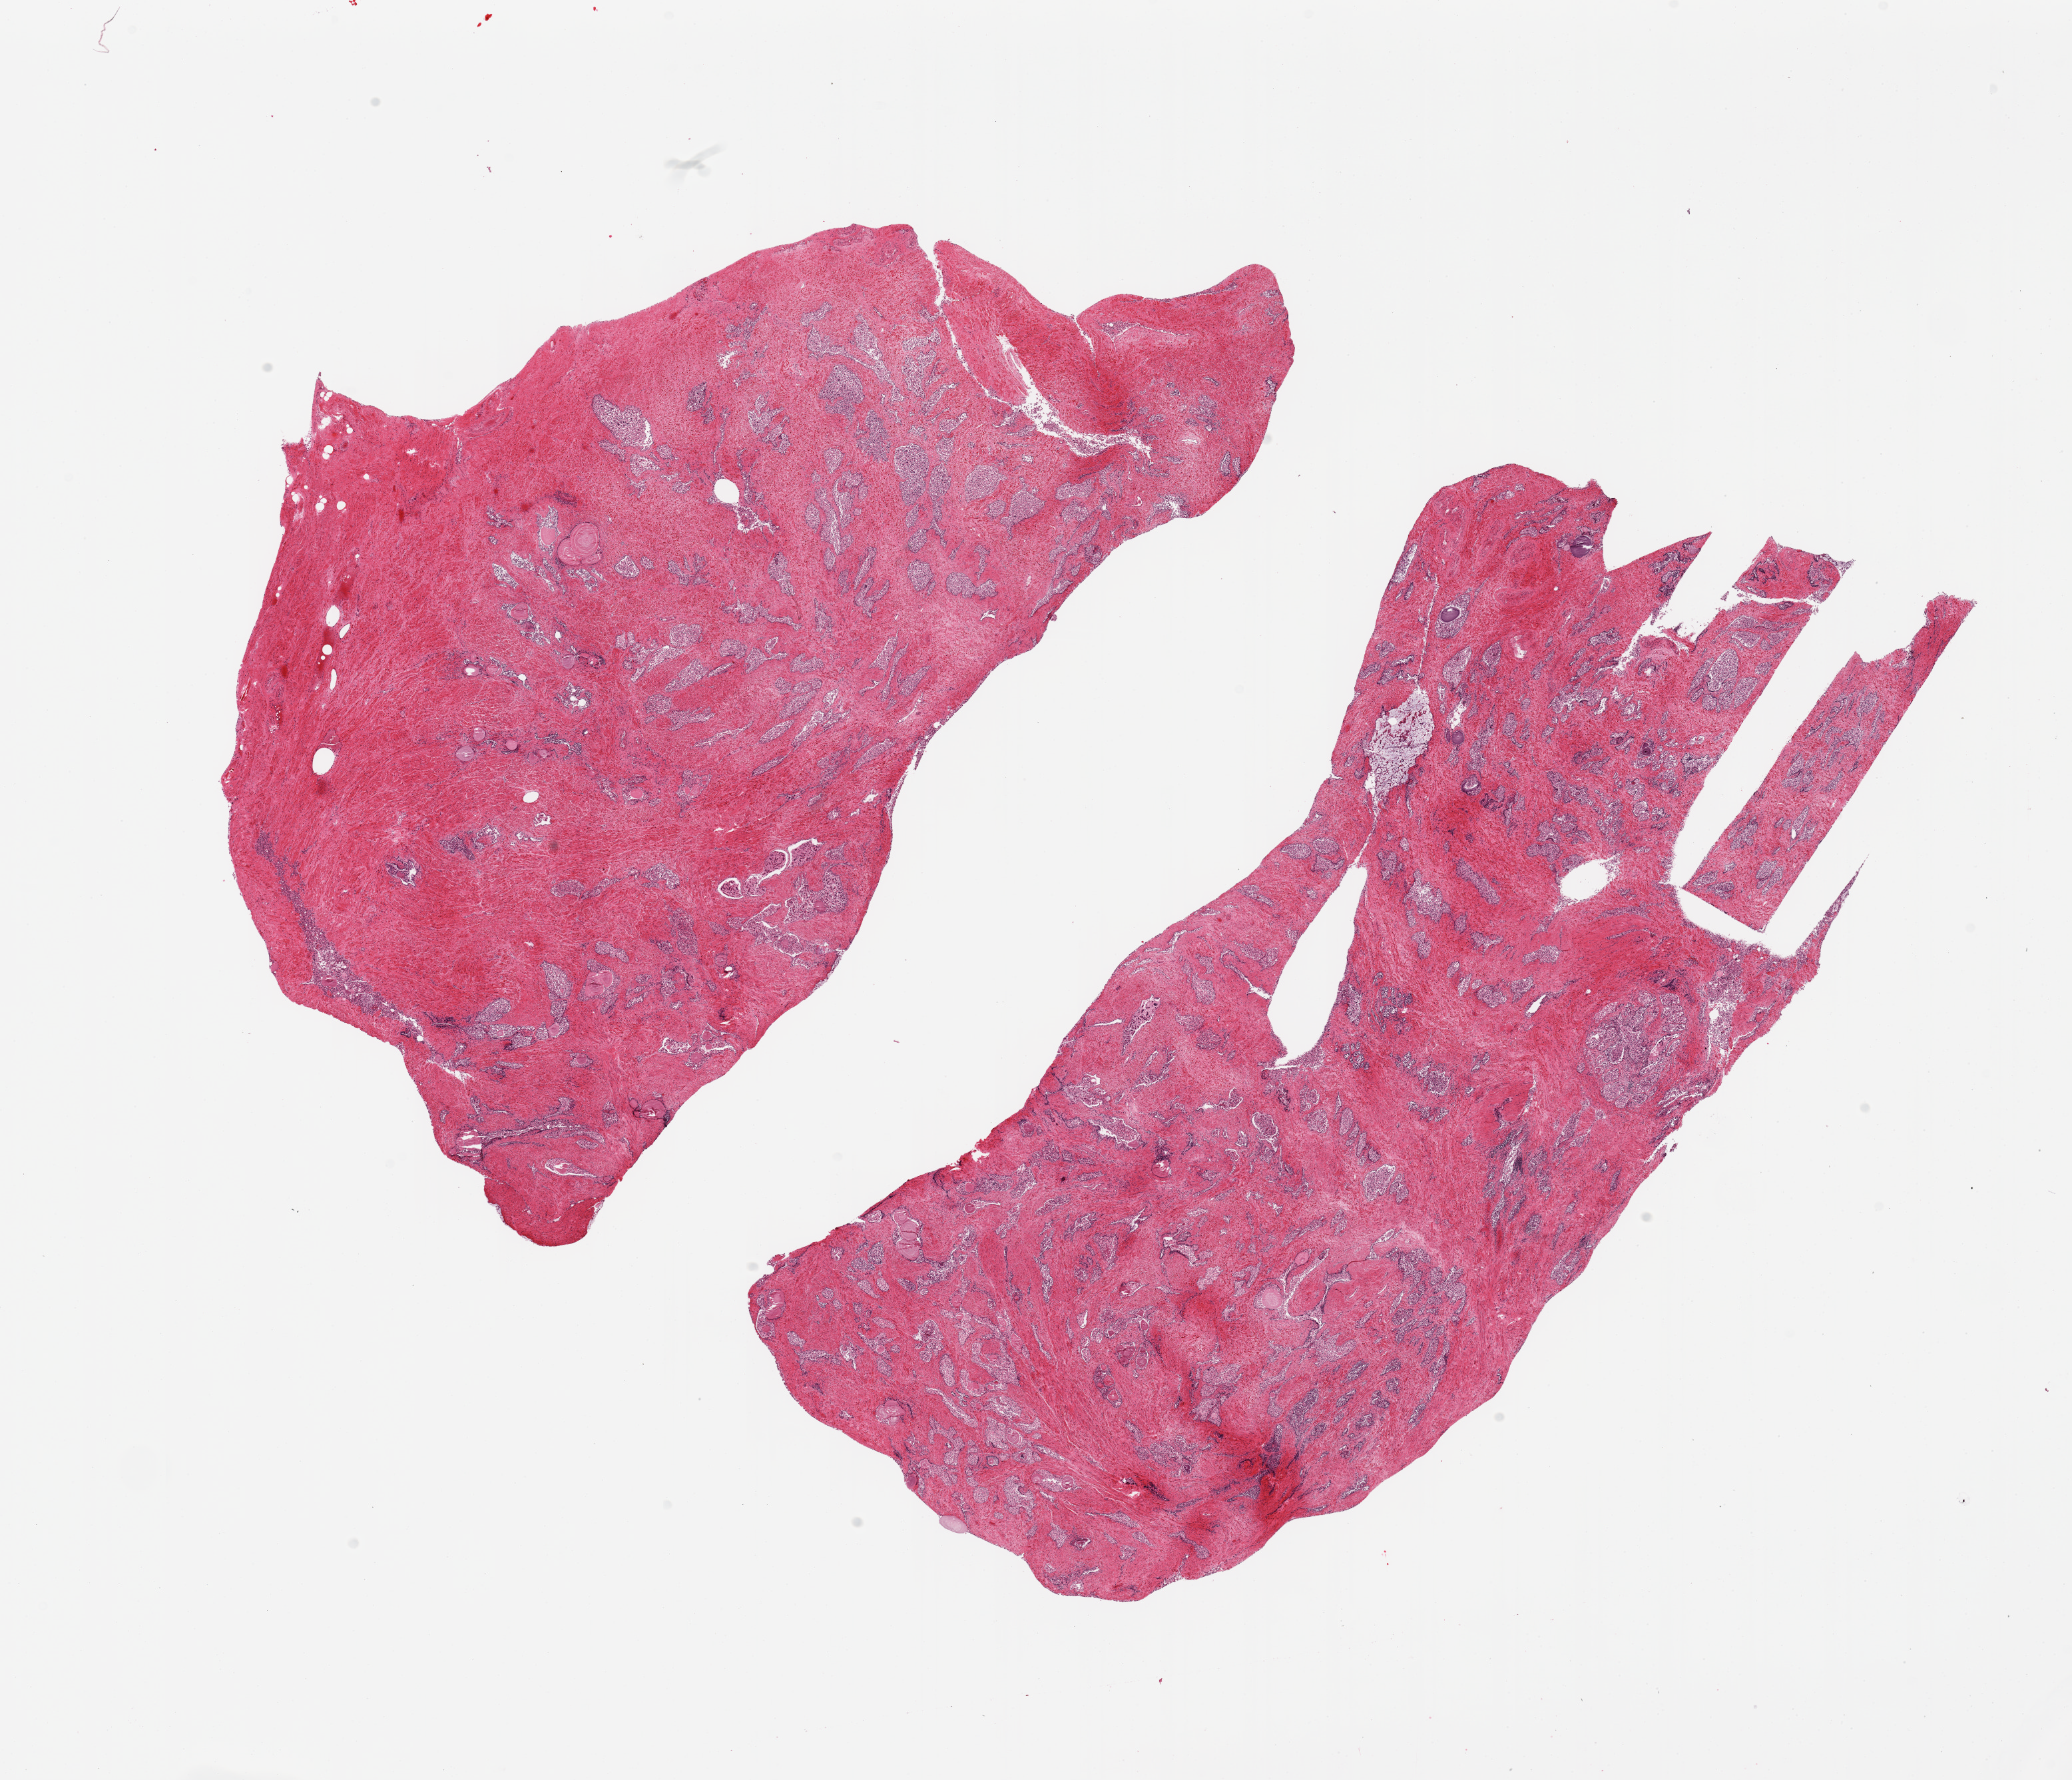
Whole-slide image, H&E stain, shown as a low-resolution overview of the whole scanned area (about 24.6 x 21.1 mm, slide scanned at 20x); PAXgene-fixed, paraffin-embedded tissue; section of prostate (target tissue); tissue donor sample. Donor sex: male.
- review note (as recorded): 2 pieces; glands autolyzed, stroma preserved